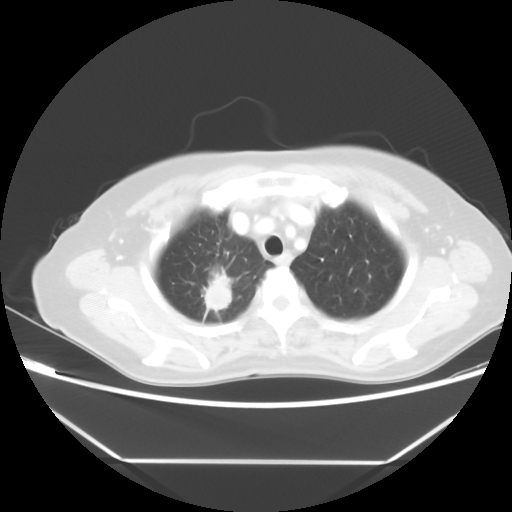
Chest CT, one axial slice. Reconstruction kernel STANDARD. 100 kVp. Lung window (W 1500 / L -600 HU). 512 × 512 image matrix. Patient: female, 65 years. Case-level facts recorded for this patient, not image findings: clinical TNM (as recorded): T1c N1 M1.
Outlined on this slice (bounding box drawn by a radiologist):
- lung tumour (recorded histology: adenocarcinoma): bounding box [x1, y1, x2, y2] px = [198, 274, 234, 316]